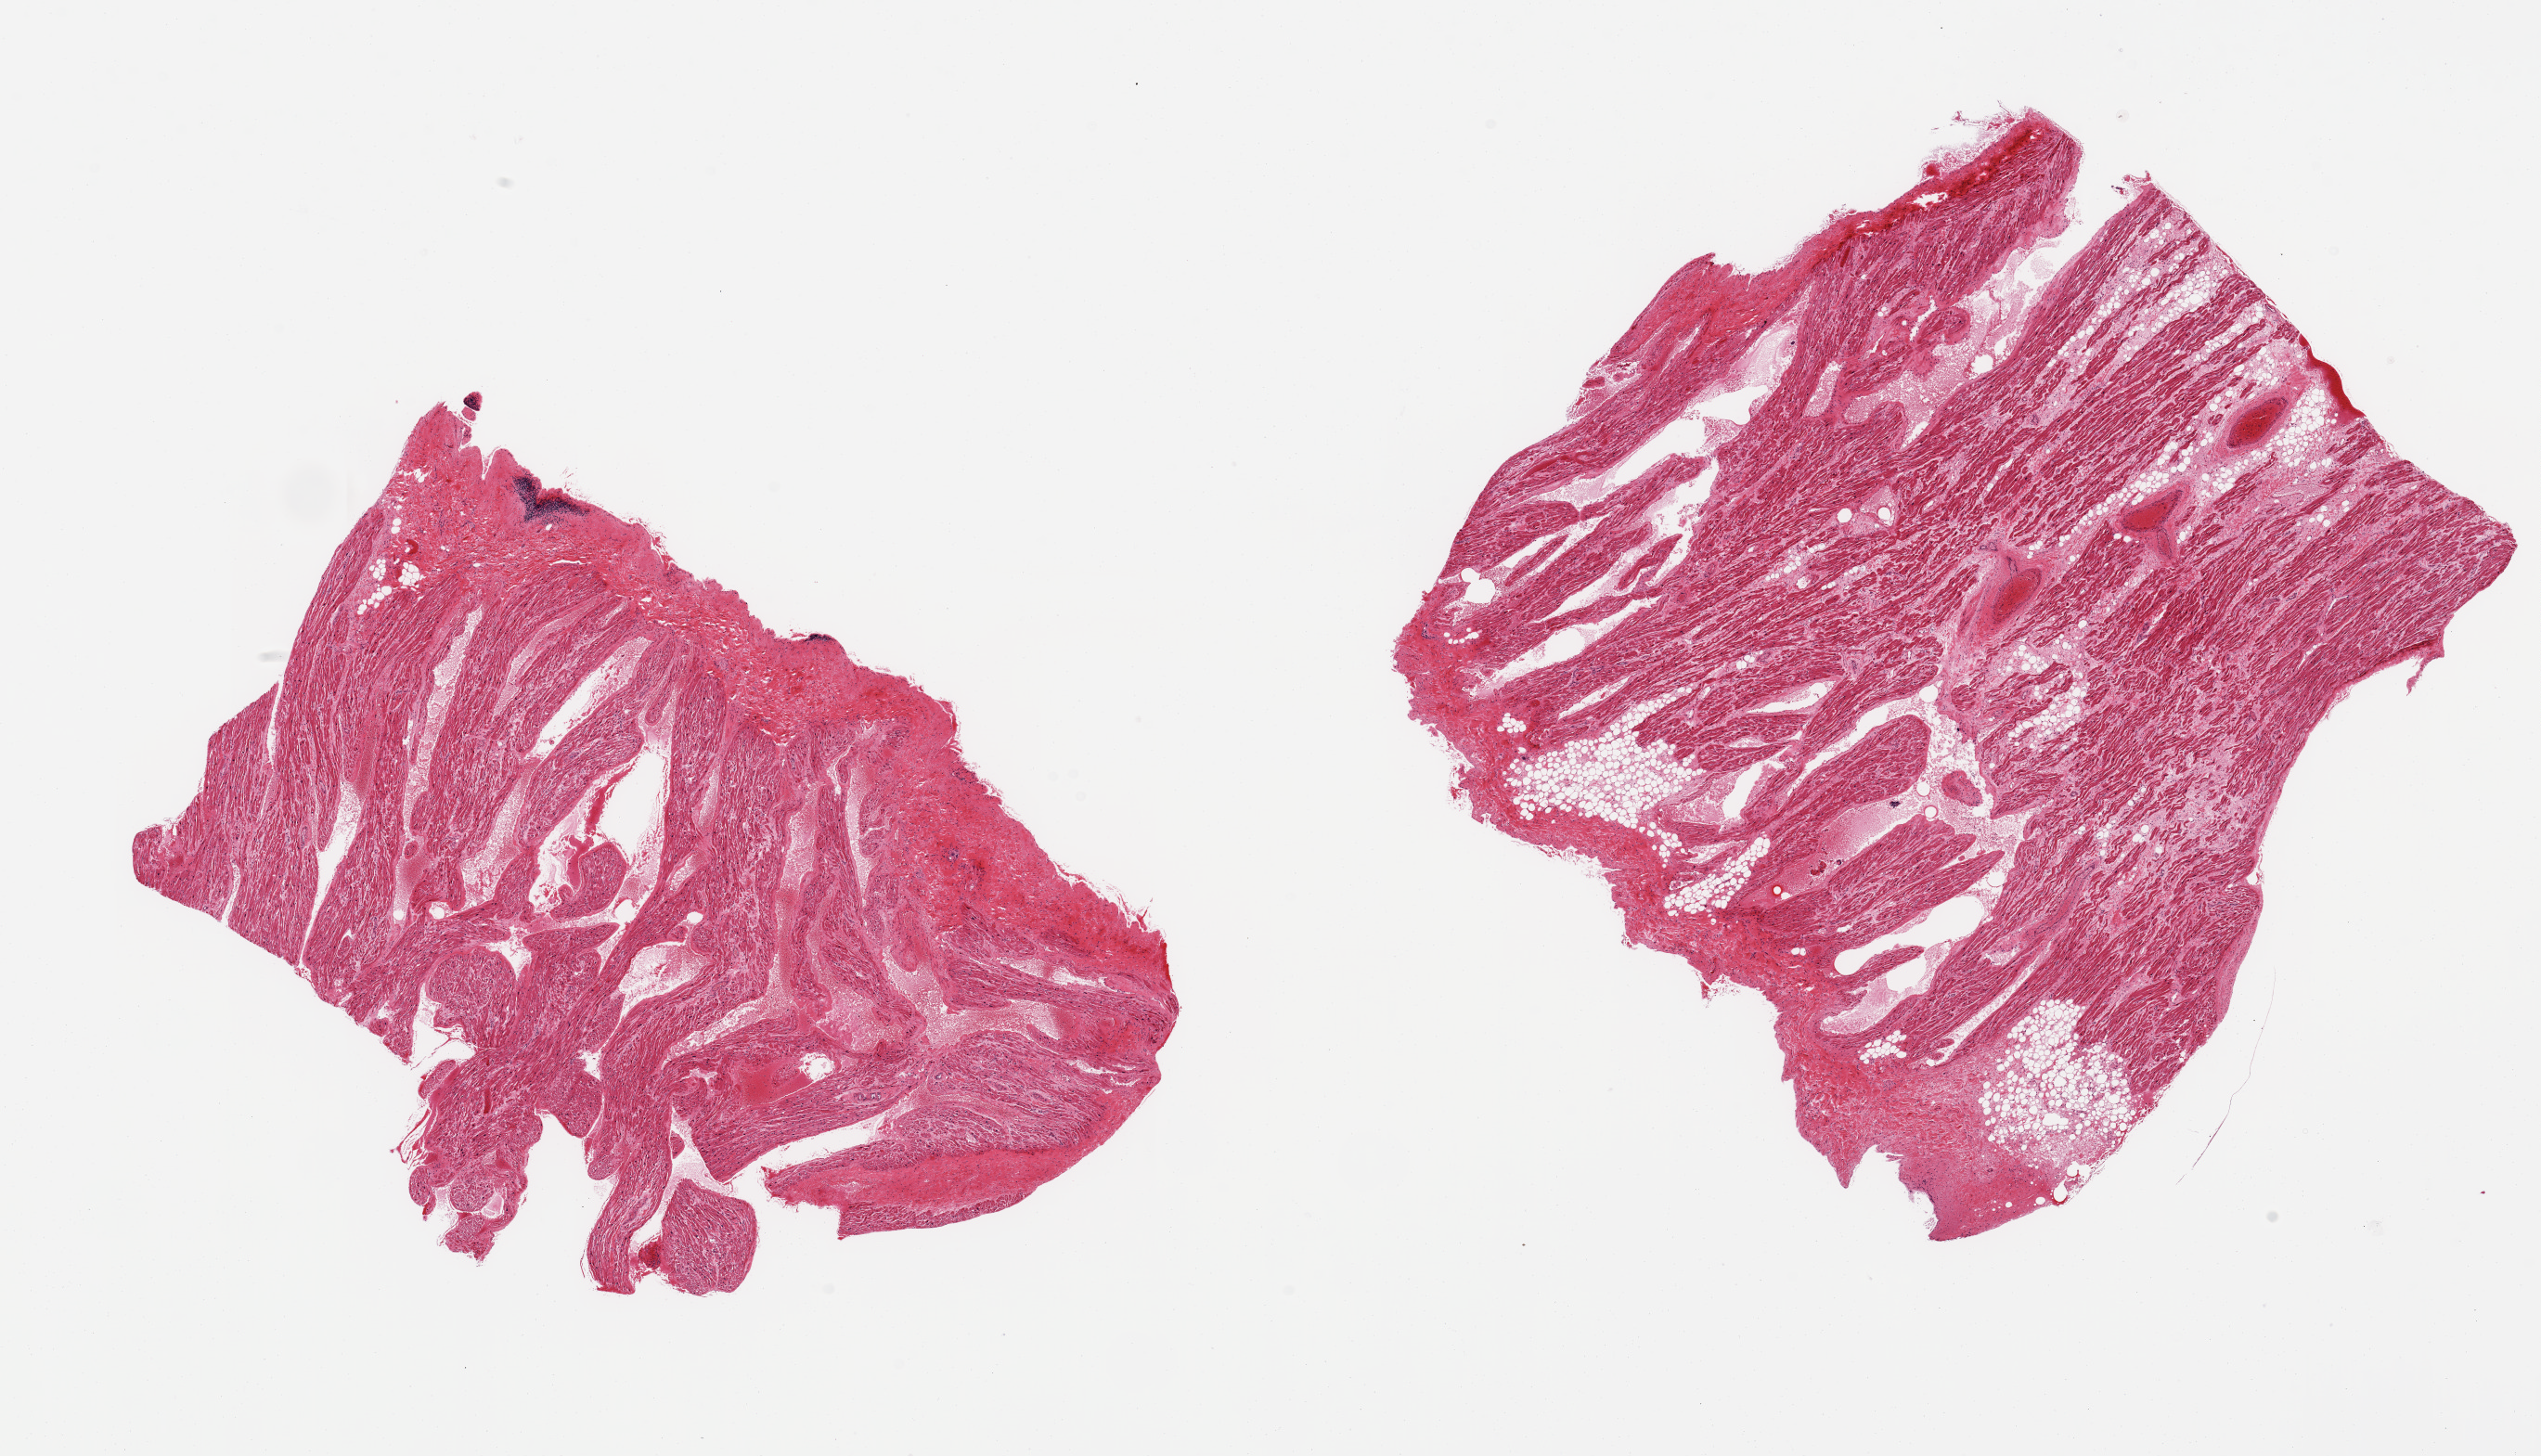
Haematoxylin and eosin whole-slide image — shown as a low-resolution overview of the whole scanned area (about 21.7 x 12.4 mm), PAXgene-fixed paraffin-embedded (PFPE) section, sampled site (target tissue): auricular appendage, tissue donor sample. Donor: male.
Reviewer comment on this tissue sample: 2 pieces; 20% fibrous content in 1, 20% fat content in other piece.